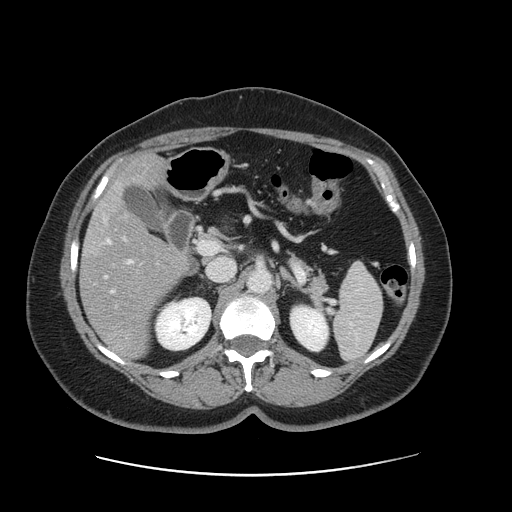
Contrast-enhanced abdominal CT, one axial slice. Position 77 of 161 along the scan axis. 120 kVp. Intravenous contrast given. Soft-tissue window (W 400 / L 40 HU). 2.5 mm slice thickness. 512 × 512 image matrix, field of view 398 × 398 mm. Female patient, age 62 years. From the clinical record (not read from this slice): diagnosis: colorectal cancer liver metastases, imaged before liver resection; multiple liver metastases: no; largest metastasis: 2.5 cm; disease in both lobes: no.
Structures marked on this image (expert manual segmentation):
- hepatic veins: bounding box (x1, y1, x2, y2) in pixels: (105, 239, 114, 293)
- liver: (82, 156, 187, 360)
- planned liver remnant (the part of the liver to remain after resection): (115, 156, 163, 191)
- portal vein (with intrahepatic branches): (123, 237, 132, 263)